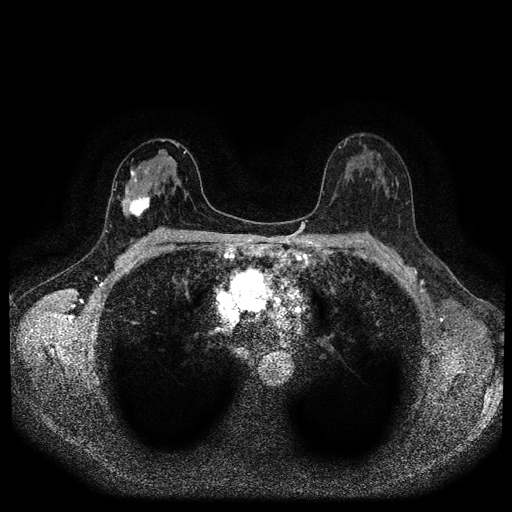
Breast MRI (dynamic contrast-enhanced, multi-phase), one axial slice. Position 61 of 116 along the scan axis. Dynamic contrast-enhanced series, time point 2 of 5 at this slice position (early post-contrast). 1.5 T. TE 2.7 ms, TR 5.4 ms. 512 × 512 image matrix, field of view 330 × 330 mm. Patient: female, 42 years.
Structures marked on this image (semi-automatic segmentation, software-assisted and operator-edited):
- breast lesion (labelled 'tumour' in the annotation; benign lesions carry a separate 'benign' label): bounding box (x1, y1, x2, y2) in pixels: (126, 194, 152, 219)